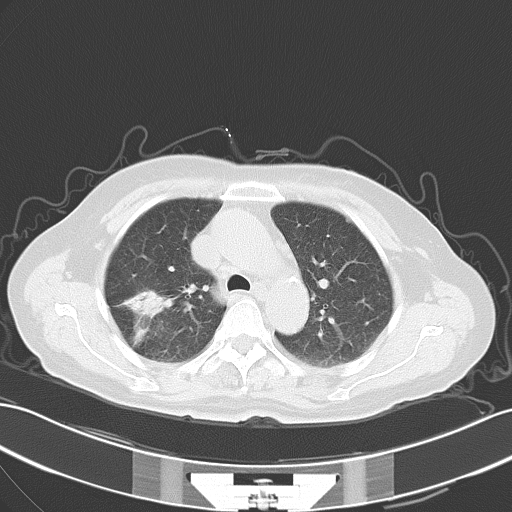
Chest CT, one axial slice; slice 41 of 57 in the series (ordered by position); 120 kVp; lung window (W 1500 / L -600 HU); 5 mm slice thickness; 512 × 512 image matrix, field of view 353 × 353 mm. Female patient, age 65 years. From the clinical record (not read from this slice): clinical TNM (as recorded): T1c N0 M1c.
Annotated regions visible in this slice (bounding box drawn by a radiologist):
- lung tumour (recorded histology: adenocarcinoma): bounding box <119,283,166,320> (left, top, right, bottom; pixels)